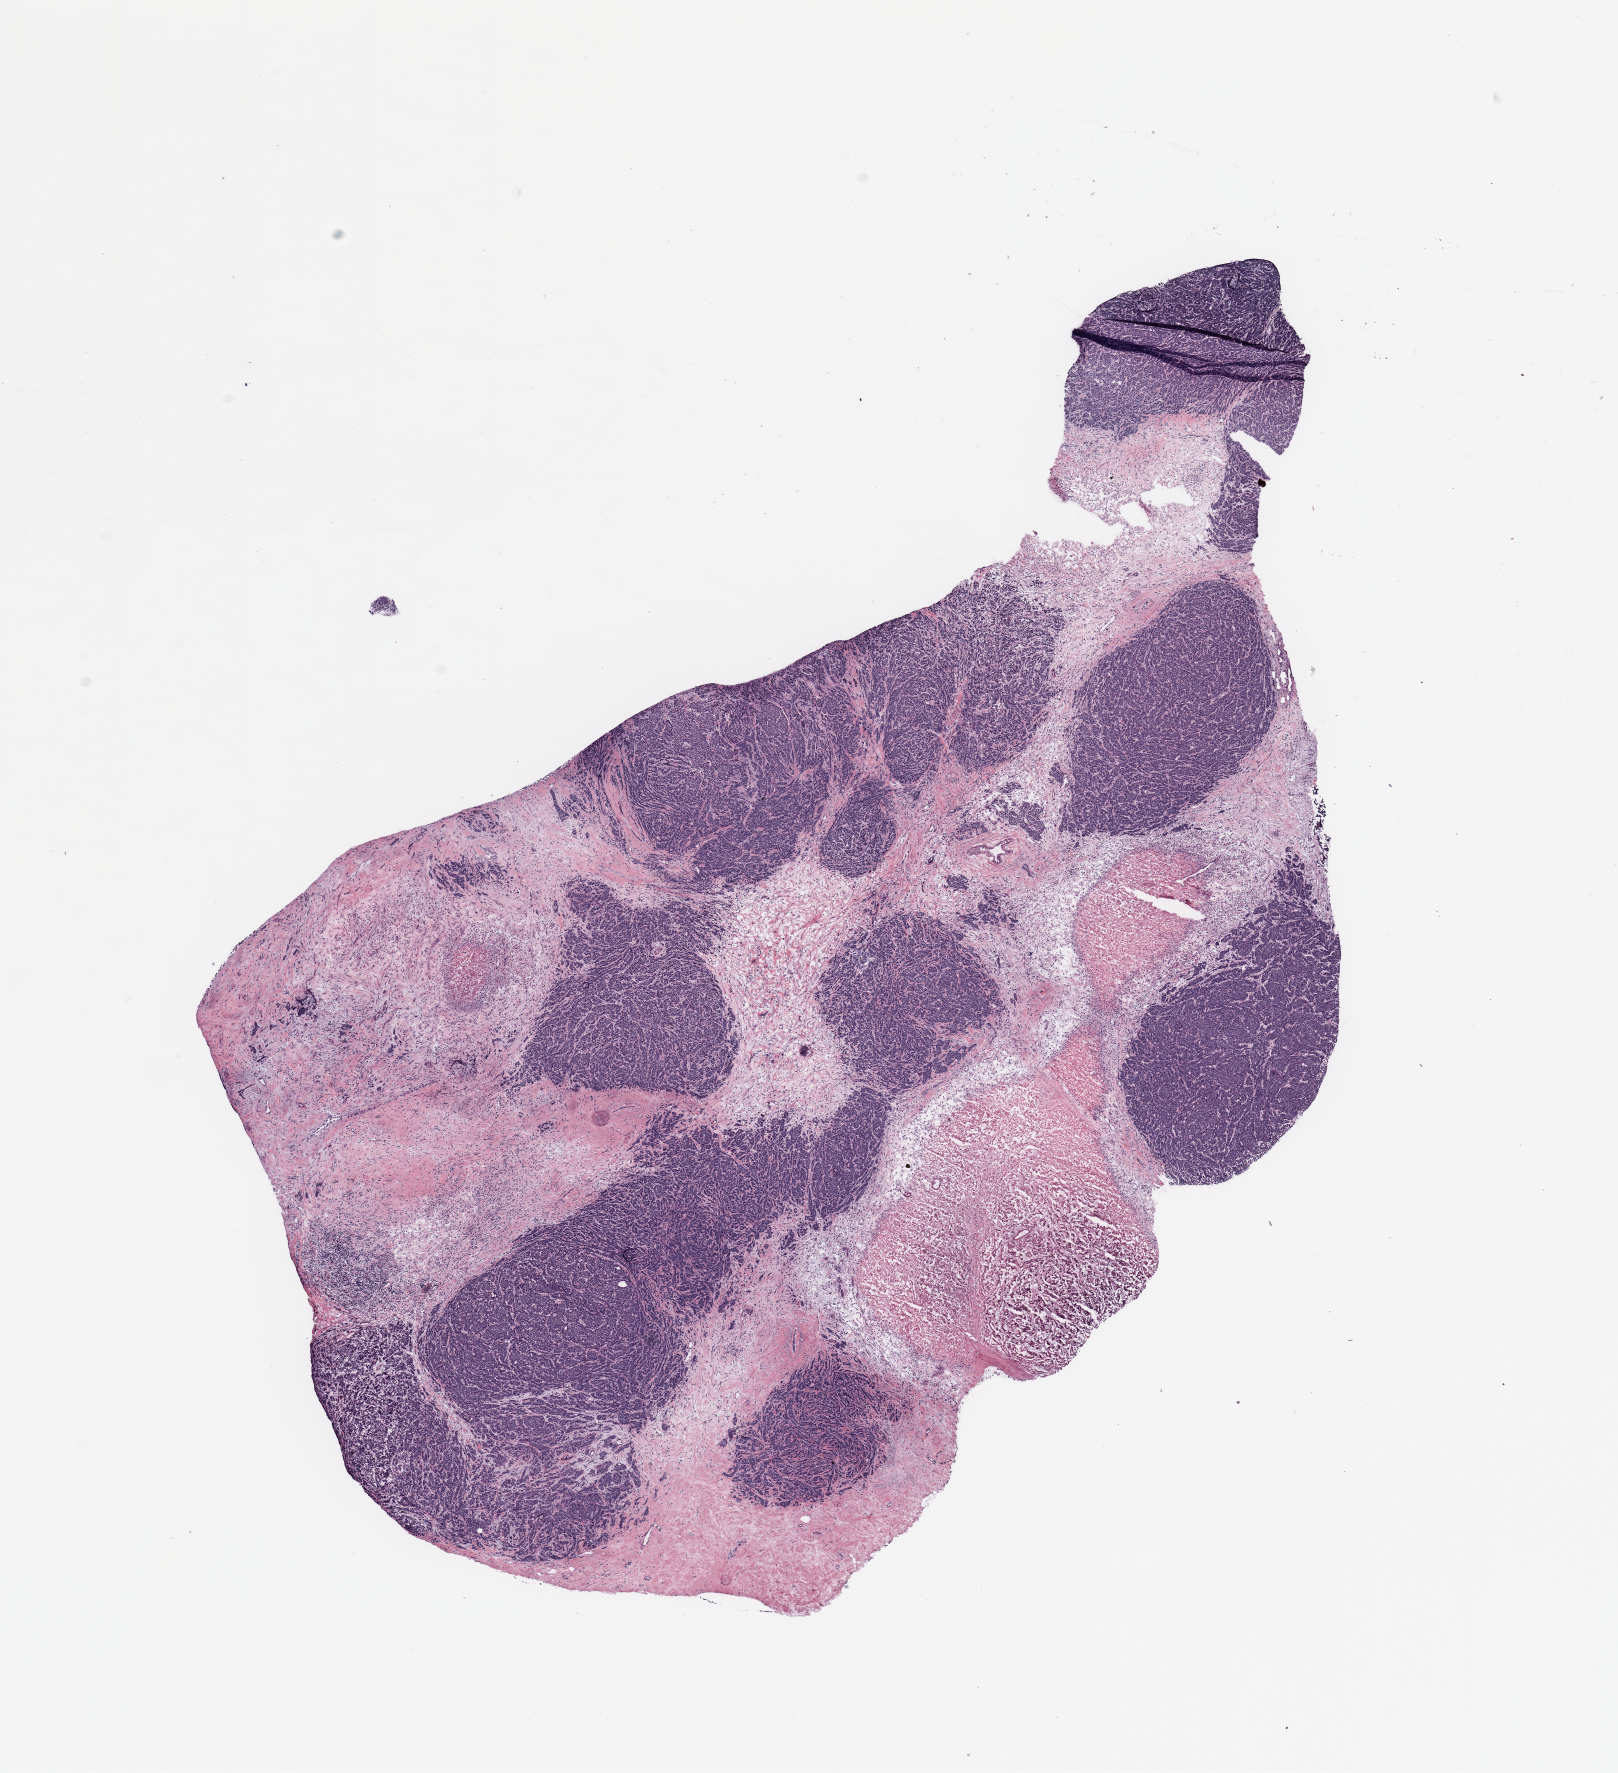
Digitized Hematoxylin and eosin (H&E) stained tissue section (whole slide) — a low-resolution overview of the entire scanned area, about 12.8 x 14.0 mm (slide scanned at 20x); tumour tissue sample, breast. Patient: female, age 78 years.
Histologic diagnosis: Infiltrating duct carcinoma, NOS. AJCC pathologic stage: IIA.